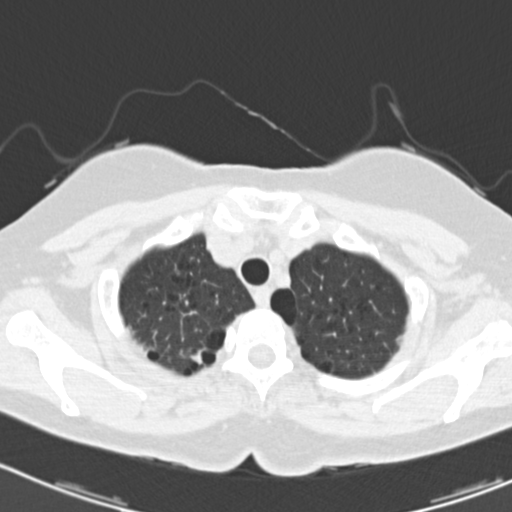
Axial slice from a low-dose chest CT screening exam; baseline annual screen; lung window (W 1500 / L -600 HU); 2 mm slice thickness; 120 kVp; slice 24 of 166 in the series; 512 × 512 image matrix. Female participant, aged 64 years at enrolment.
Expert-annotated lung lesion, bounding box <177,335,222,379> (left, top, right, bottom; pixels). No non-calcified nodule or mass ≥4 mm was recorded by the screening reader at this exam. Later outcome: lung cancer diagnosed 402 days after this screen — adenocarcinoma, NOS, right upper lobe, poorly differentiated (G3), stage IB (AJCC 6th edition), 15 mm at pathology.